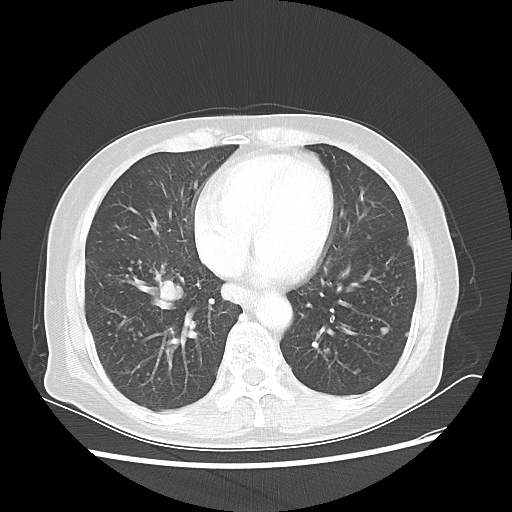
Chest CT, one axial slice. Position 20 of 56 along the scan axis. Reconstruction kernel LUNG. Lung window (W 1500 / L -600 HU). 5 mm slice thickness. 512 × 512 image matrix. Female patient, age 68 years. From the clinical record (not read from this slice): clinical TNM (as recorded): T1c N3 M0.
Structures marked on this image (rectangle marked by the reading radiologist):
- lung tumour (recorded histology: squamous cell carcinoma): bounding box [x1, y1, x2, y2] px = [143, 265, 189, 316]